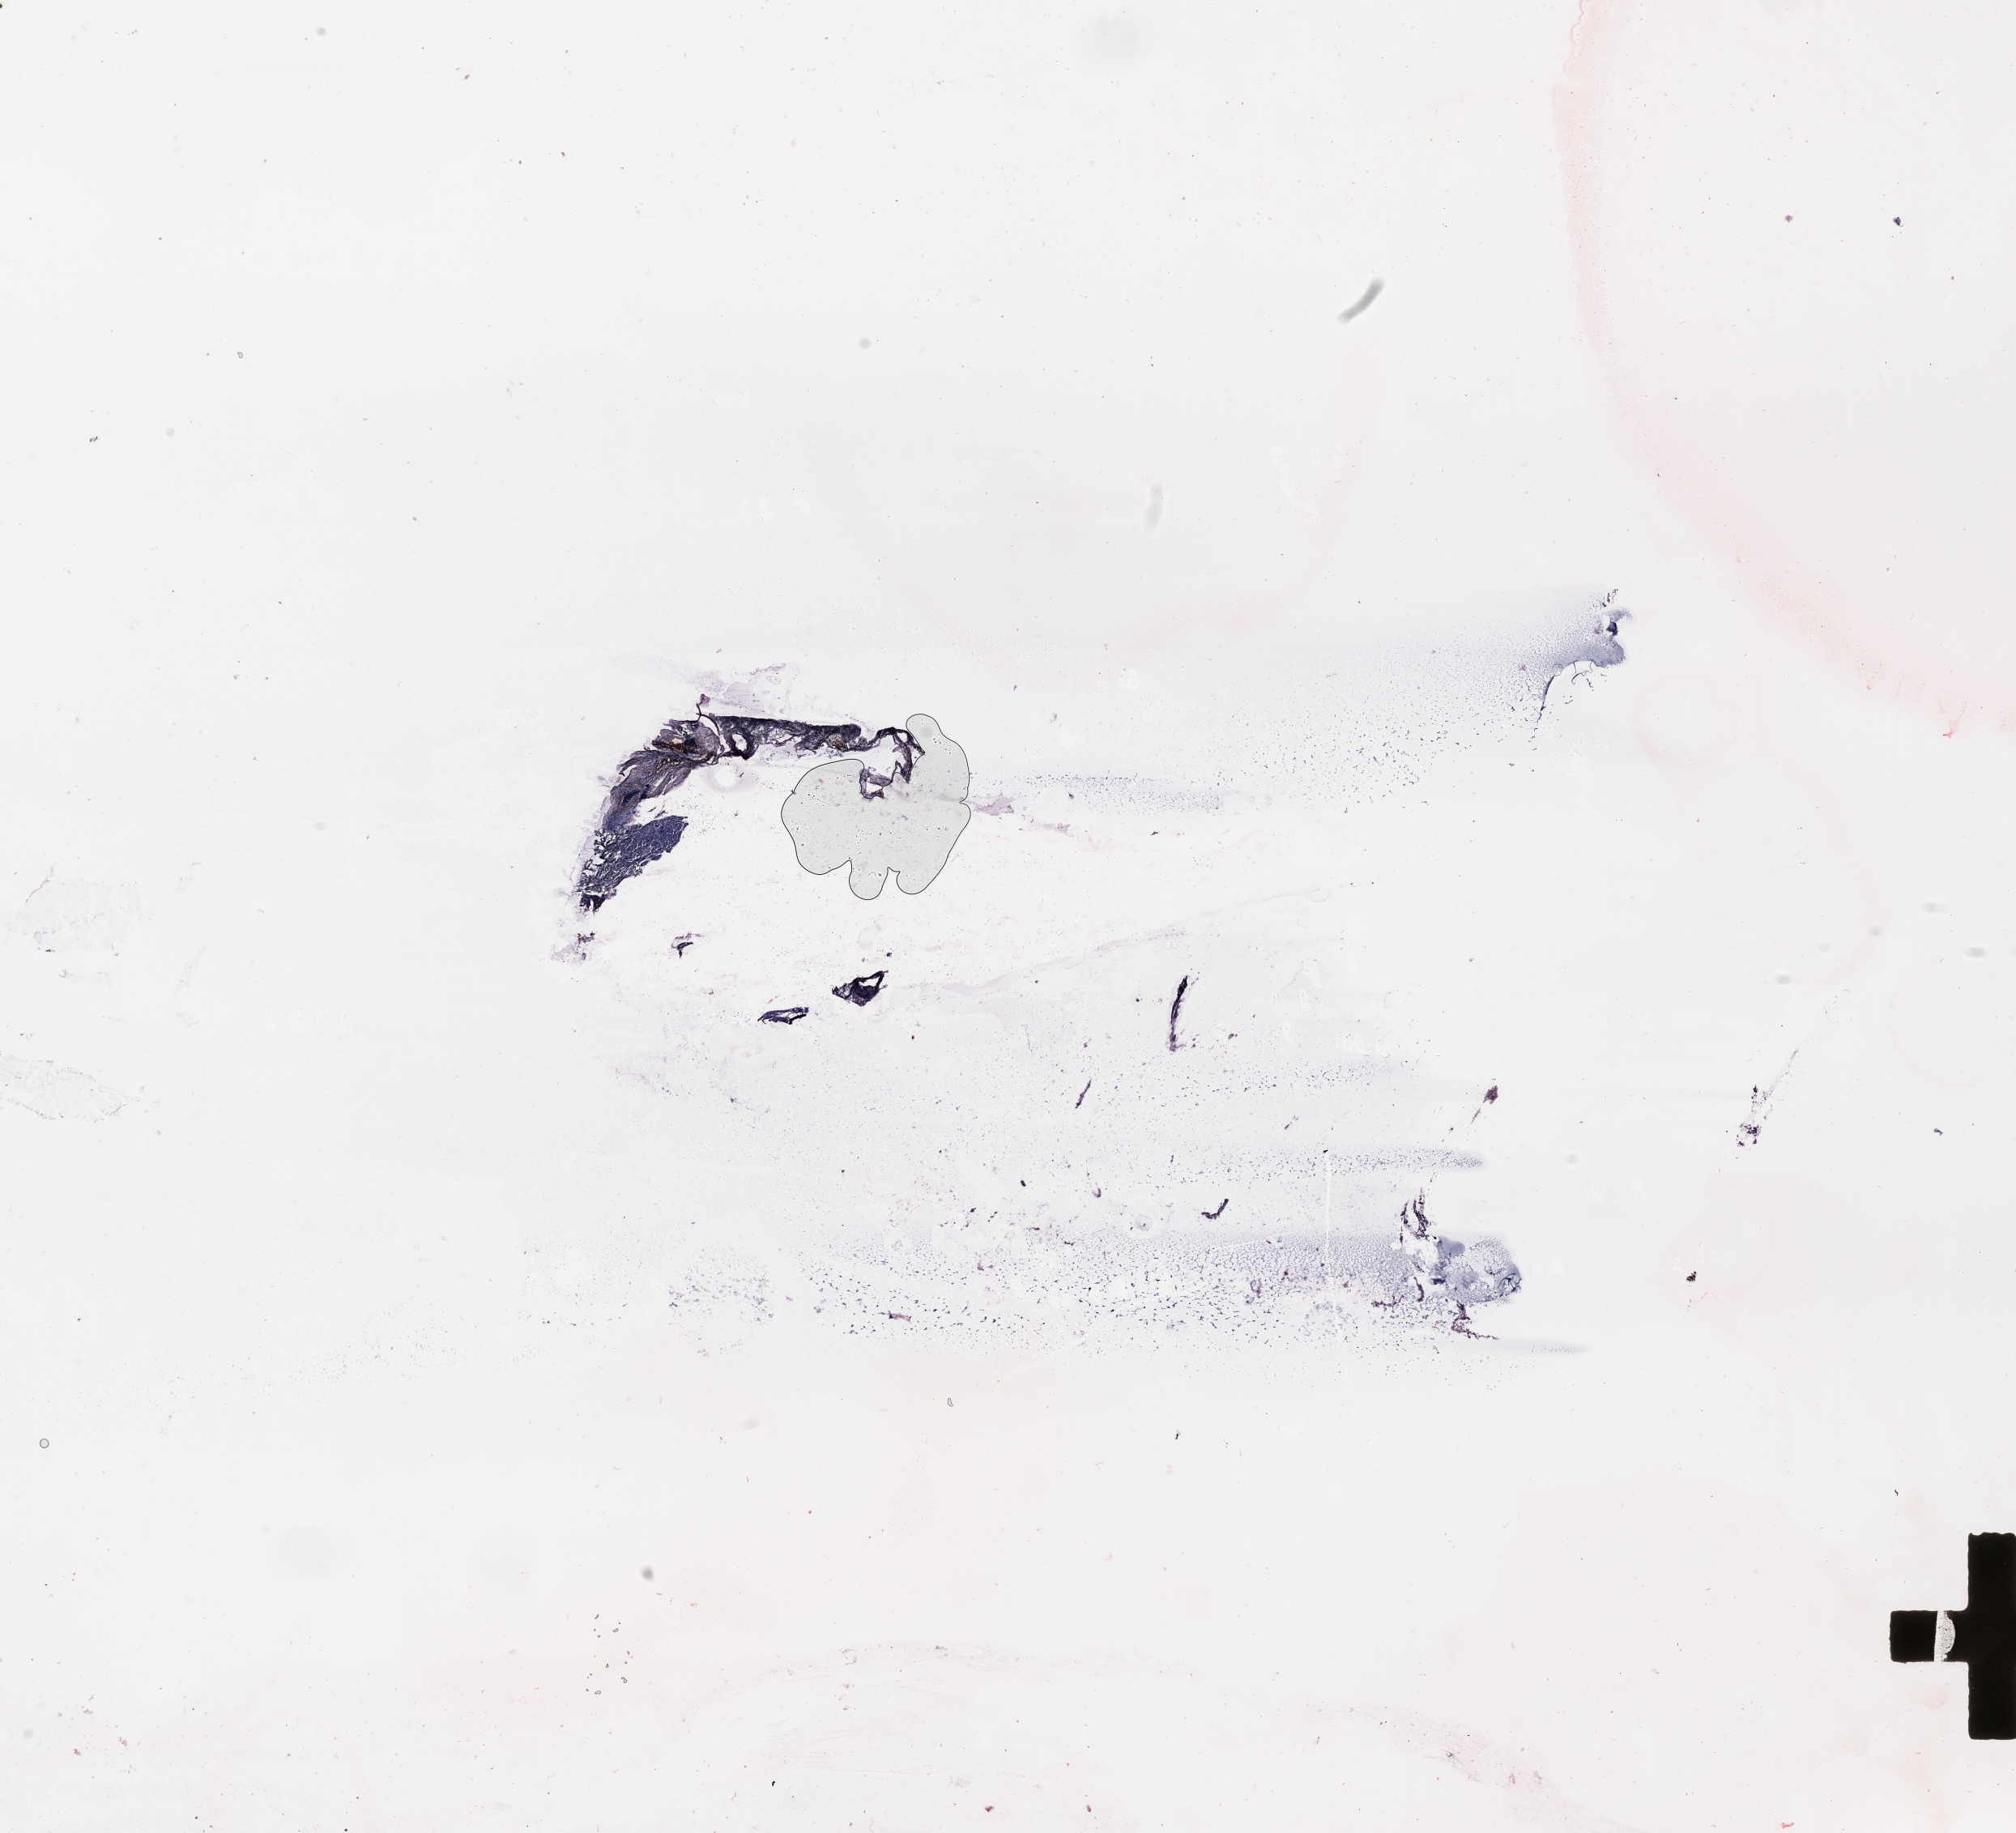
H&E-stained whole-slide image — shown as a low-resolution overview of the whole scanned area (about 19.7 x 17.9 mm, from a 20x scan); normal (non-tumour) tissue sample, uterus. Patient: female, age 66 years.
This section: normal (non-tumour) tissue from the same patient. Patient diagnosis: Endometrioid adenocarcinoma, NOS.